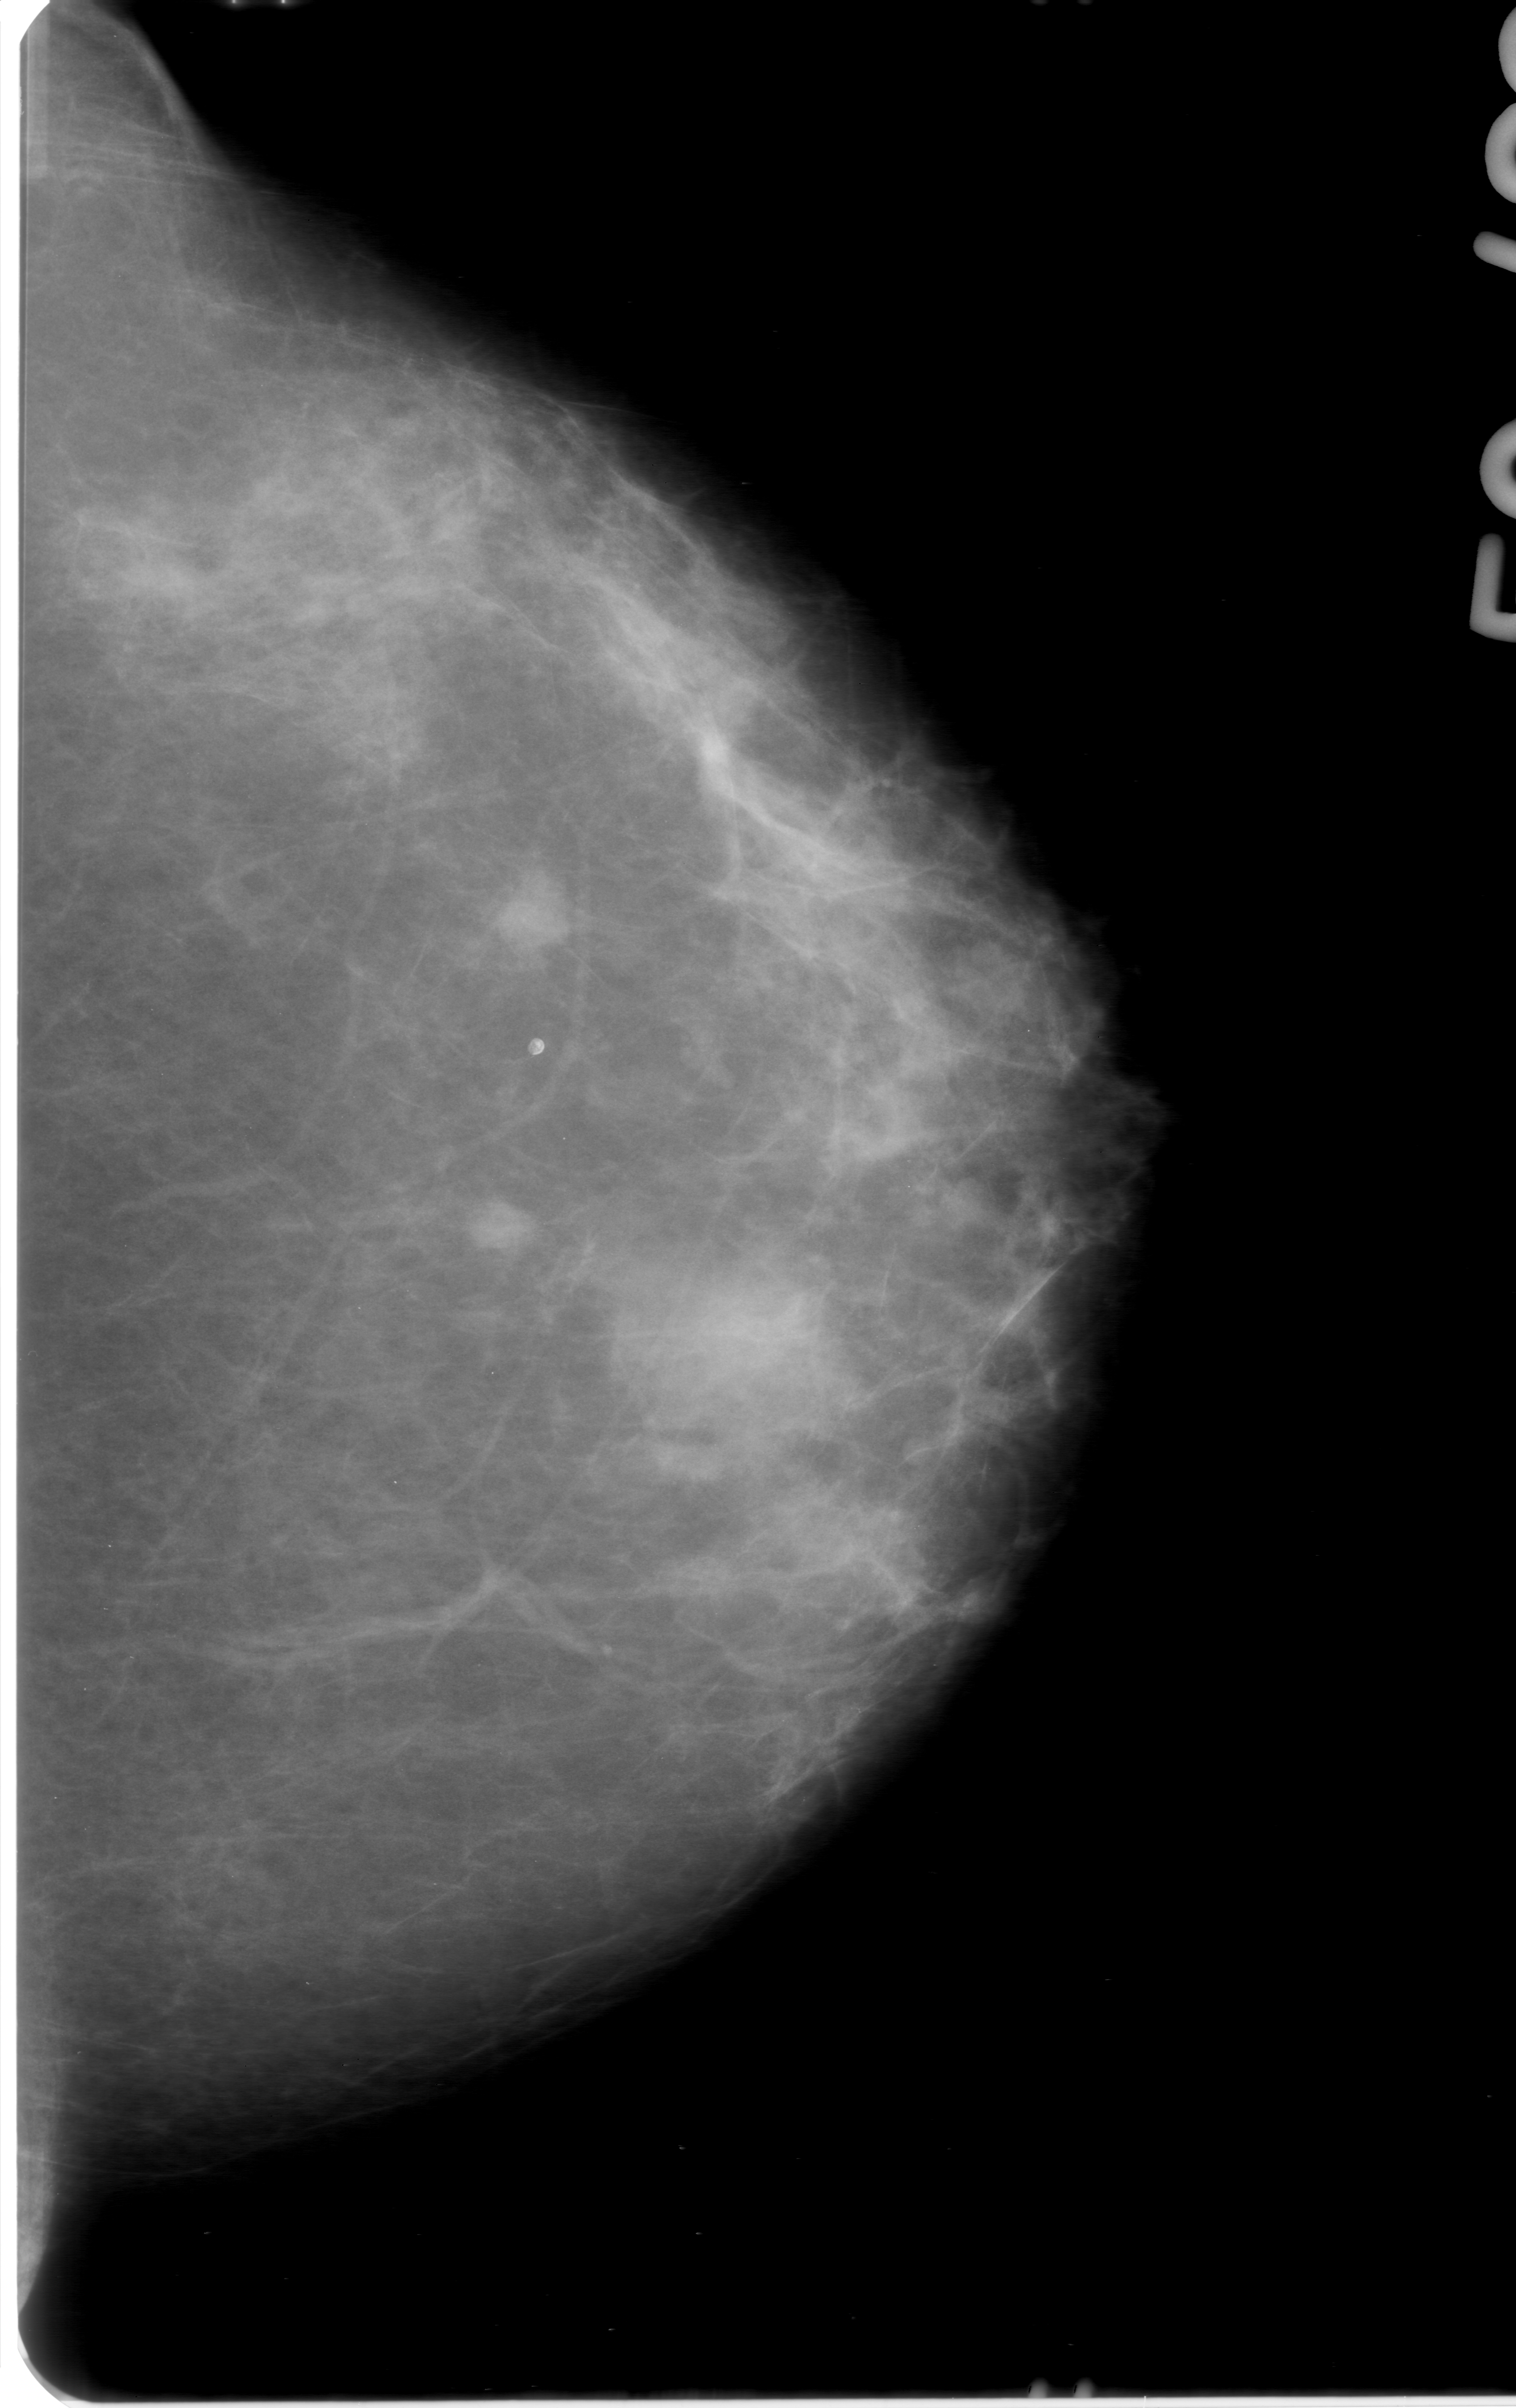
Mammogram (digitized film); left breast; craniocaudal (CC) view; BI-RADS breast density category 2 (scale 1–4).
Mass, shape oval, margins obscured; BI-RADS assessment category 0; pathology (as recorded): benign.